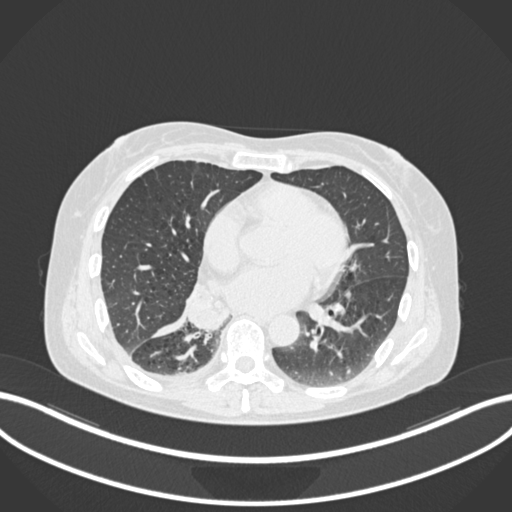
Chest CT, one axial slice; slice 69 of 168 in the series (ordered by position); lung window (W 1500 / L -600 HU); 512 × 512 image matrix. Female patient, age 63 years. Case-level facts recorded for this patient, not image findings: clinical TNM (as recorded): T1c N0 M0.
Structures marked on this image (rectangle marked by the reading radiologist):
- lung tumour (recorded histology: adenocarcinoma): bounding box (x1, y1, x2, y2) in pixels: (183, 282, 232, 332)